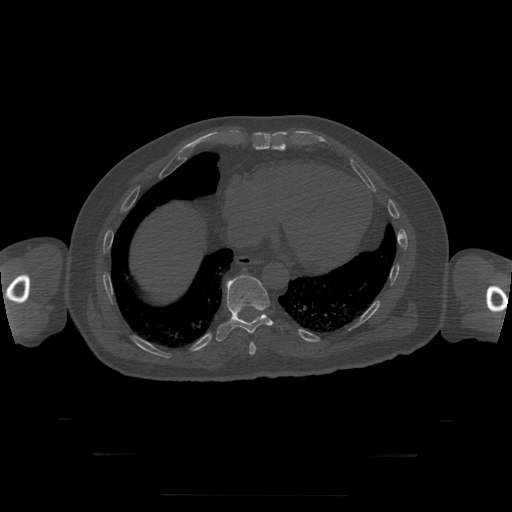
CT including the spine, one axial slice. Slice 124 of 397 in the series (ordered by position). Bone window (W 1800 / L 400 HU). 1.25 mm slice thickness. 512 × 512 image matrix, field of view 510 × 510 mm. Patient age 73 years. From the clinical record (not read from this slice): primary cancer: prostate.
Annotated regions visible in this slice (semi-automatic segmentation, software-assisted and operator-edited):
- T10 vertebra: box from (x=216, y=275) to (x=274, y=342) px
- T9 vertebra: (x=249, y=342)–(x=256, y=355)